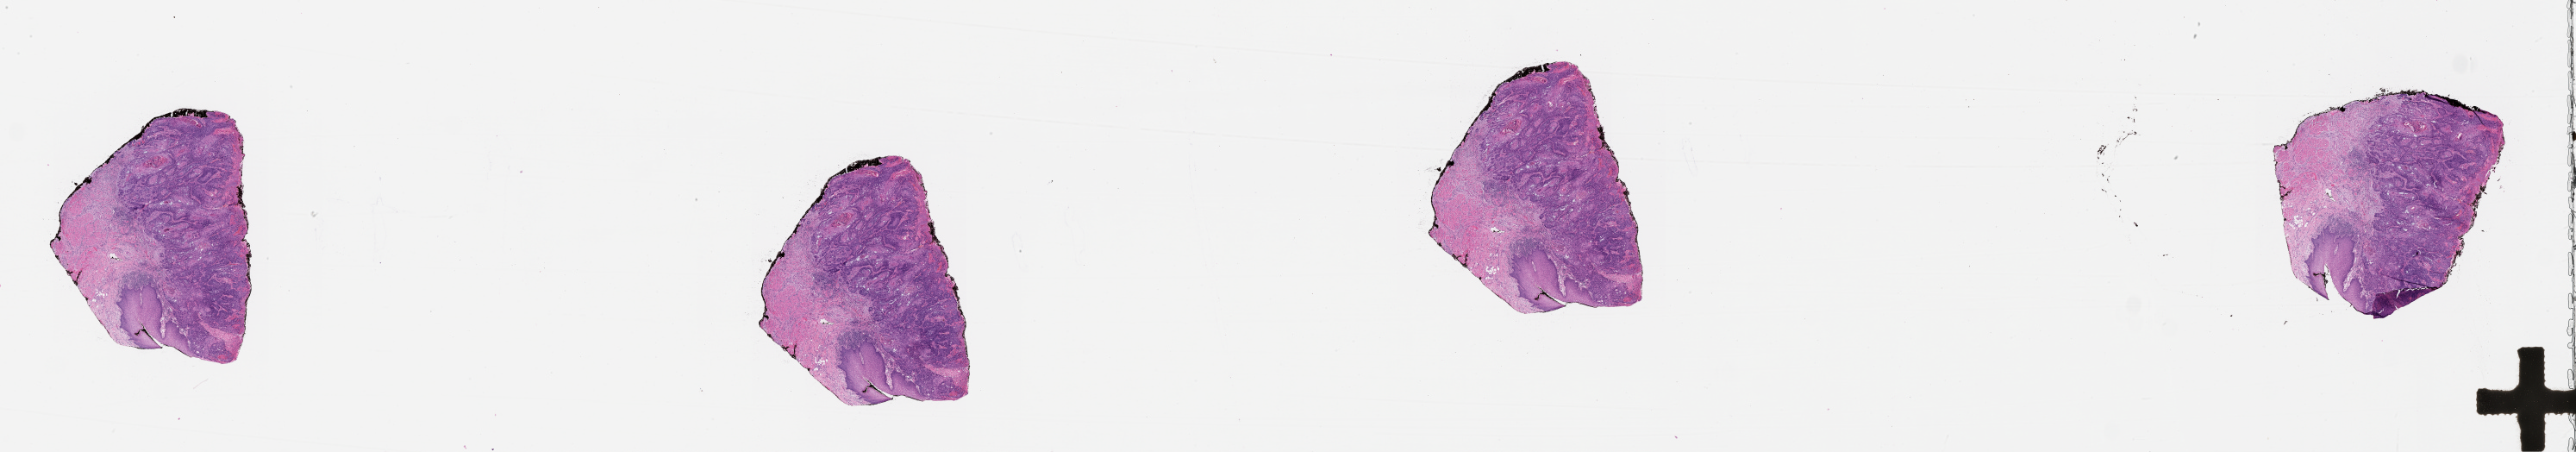
Whole-slide histology image, H&E, low-resolution overview of the scanned area, about 48.1 x 8.4 mm. Head and neck, tissue type not recorded. Male, 63 y/o.
Patient diagnosis: Squamous cell carcinoma, NOS (floor of mouth, NOS).